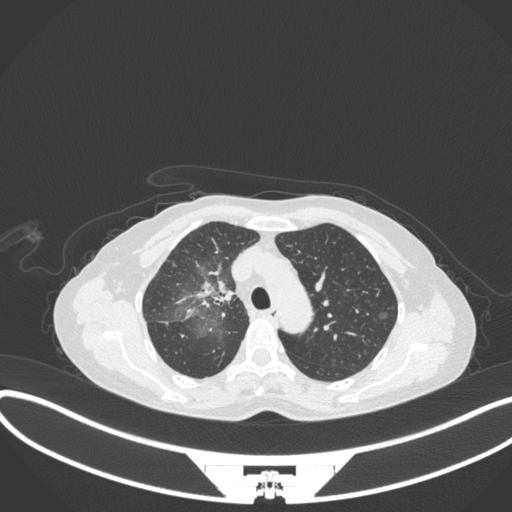
Chest CT, one axial slice. Position 229 of 311 along the scan axis. Reconstruction kernel B31f. Lung window (W 1500 / L -600 HU). 1 mm slice thickness. 512 × 512 image matrix, field of view 400 × 400 mm. Female patient, age 59 years. From the clinical record (not read from this slice): clinical TNM (as recorded): T3 N0 M0; histopathological grade: G1.
Structures marked on this image (rectangle marked by the reading radiologist):
- lung tumour (recorded histology: adenocarcinoma): bounding box <189,268,232,308> (left, top, right, bottom; pixels)